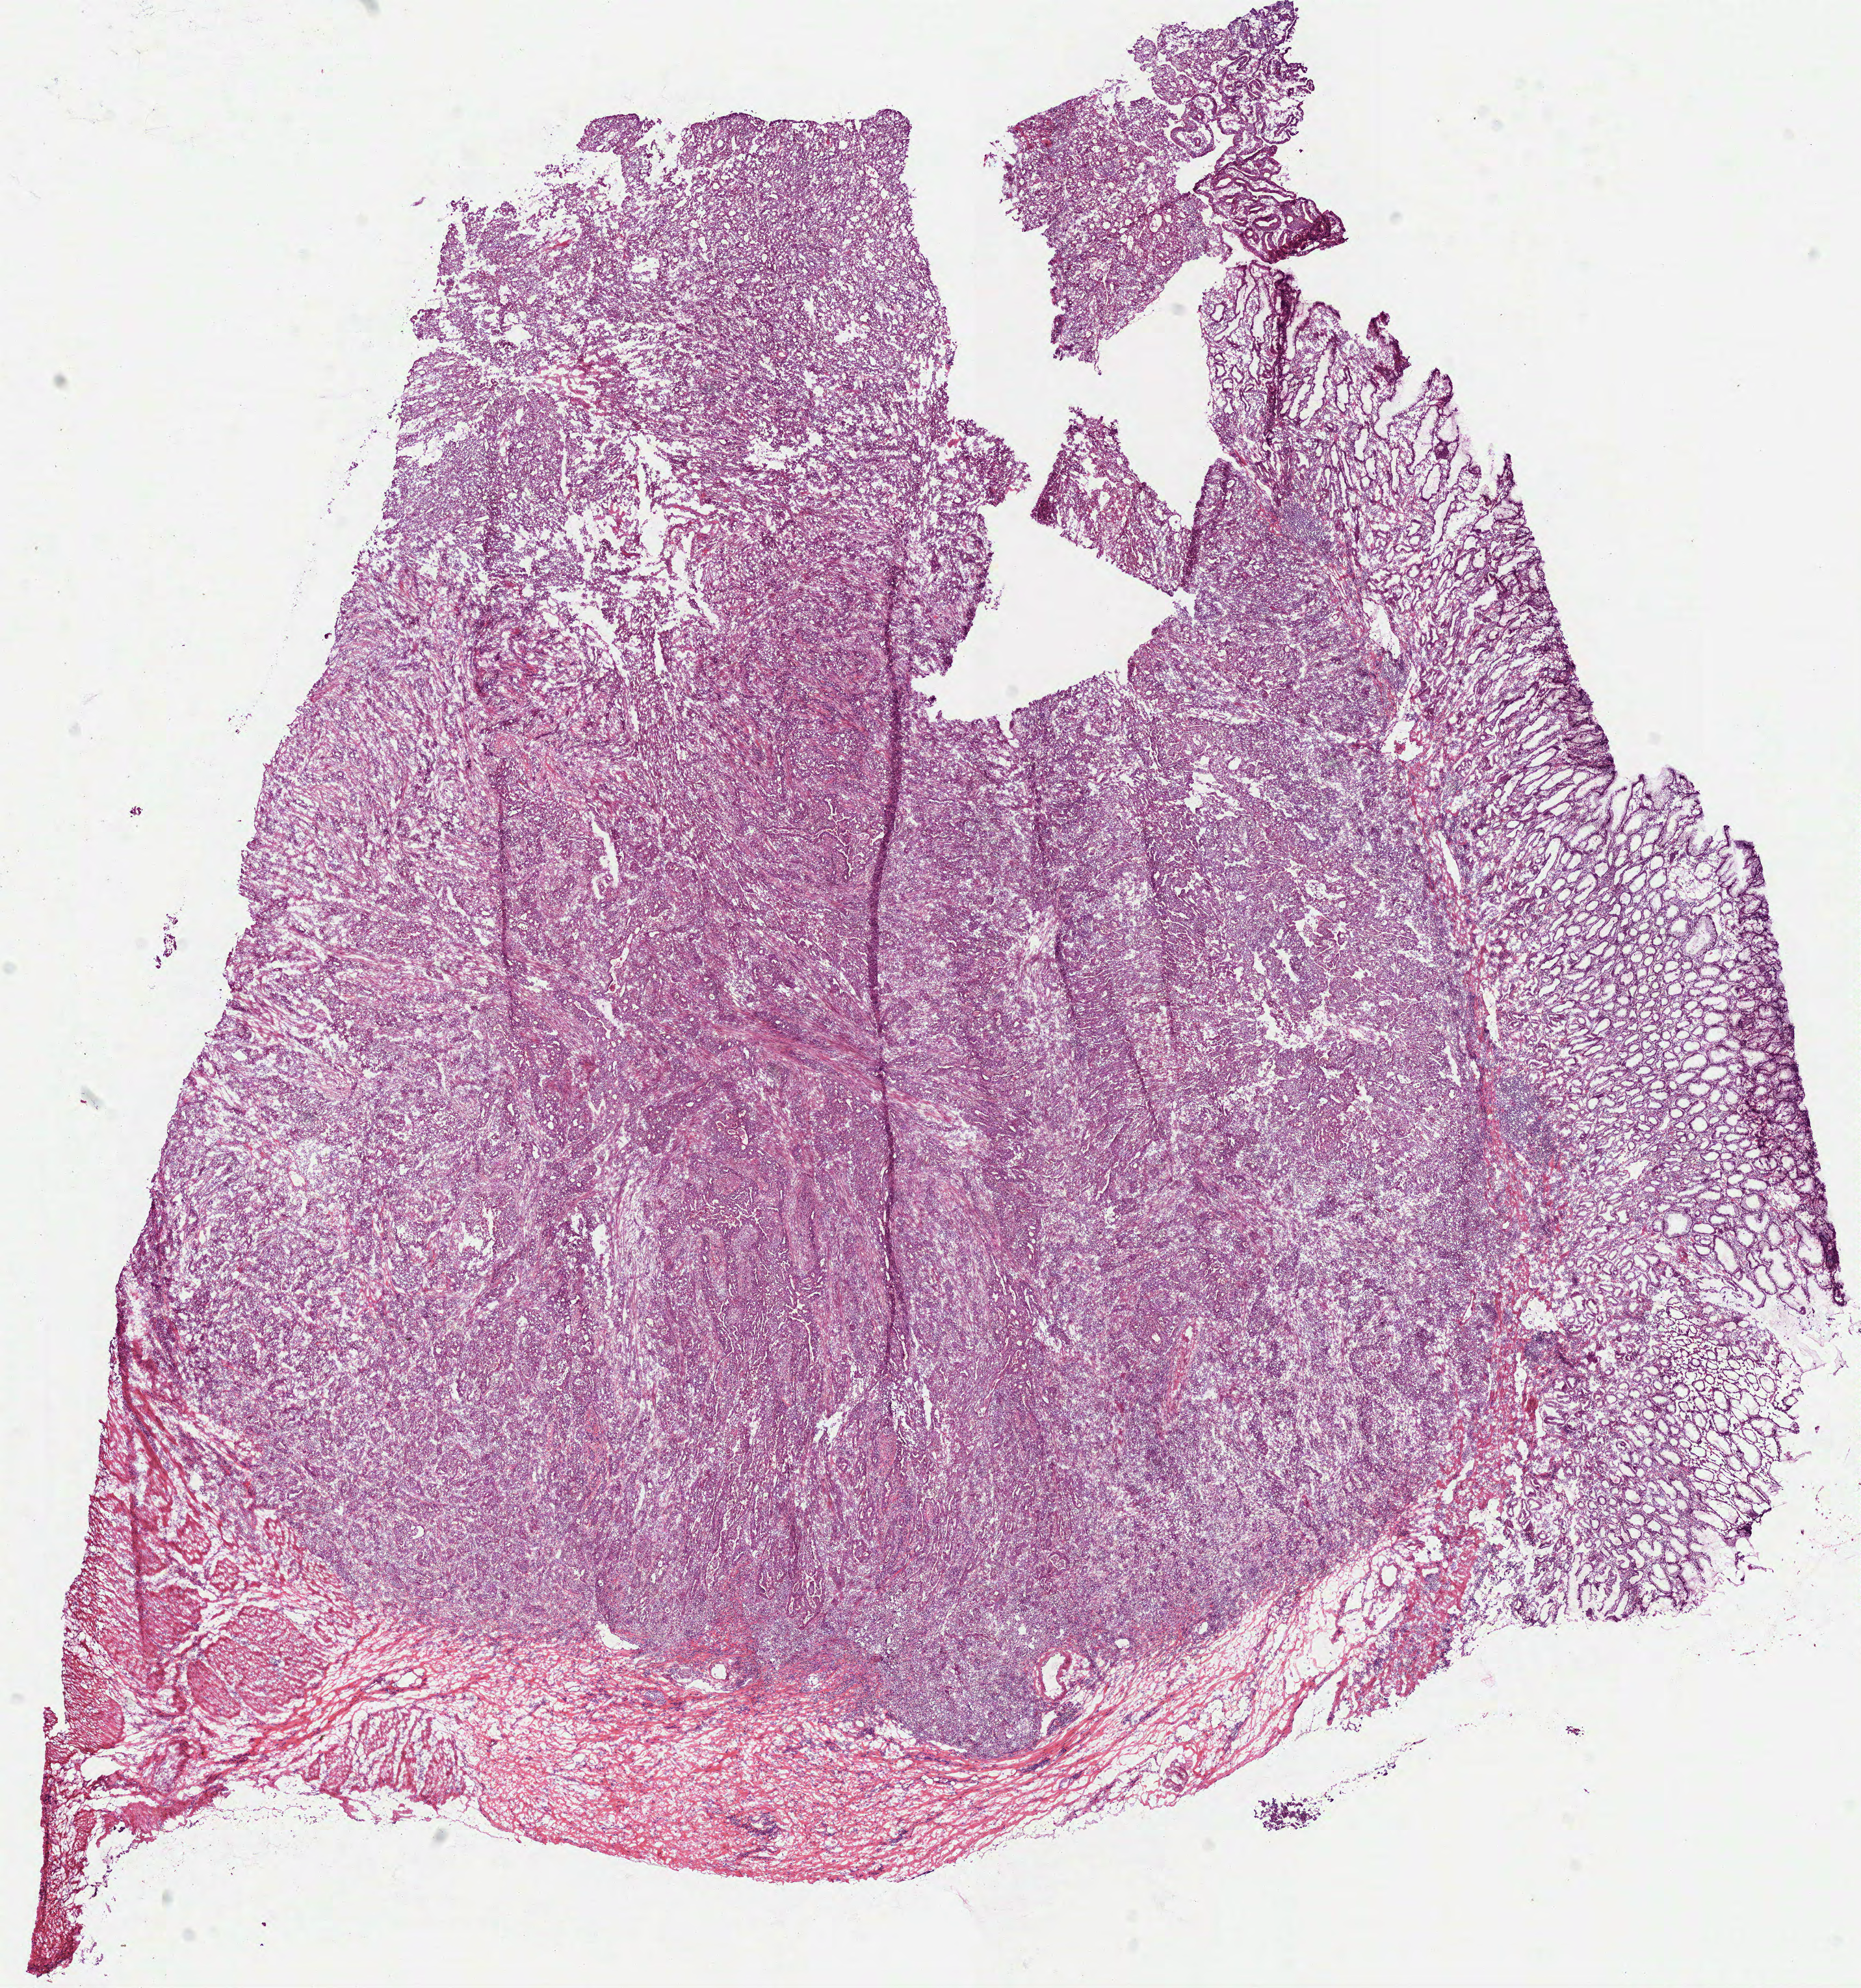
Digitized H&E tissue section (whole slide), shown as a low-resolution overview of the whole scanned area (about 11.5 x 12.3 mm); frozen section; stomach, primary tumour sample. Male patient; age at initial diagnosis 74 years. Histologic grade: G3 (poorly differentiated). Pathologist review of this section (percent, as recorded): tumour cells 78%, tumour nuclei 75%, normal cells 10%, stromal cells 10%, necrosis 2%.
AJCC pathologic stage: II. Pathologic diagnosis: Adenocarcinoma, NOS (fundus of stomach).